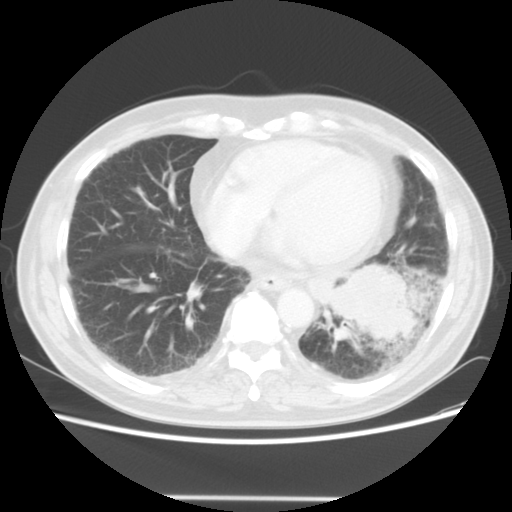
Chest CT, one axial slice. Position 16 of 56 along the scan axis. 140 kVp. Lung window (W 1500 / L -600 HU). 5 mm slice thickness. 512 × 512 image matrix. Patient: male, 66 years. Case-level facts recorded for this patient, not image findings: clinical TNM (as recorded): T4 N3 M0; histopathological grade: G3.
Annotated regions visible in this slice (bounding box drawn by a radiologist):
- lung tumour (recorded histology: small cell carcinoma): bounding box (x1, y1, x2, y2) in pixels: (325, 259, 420, 350)